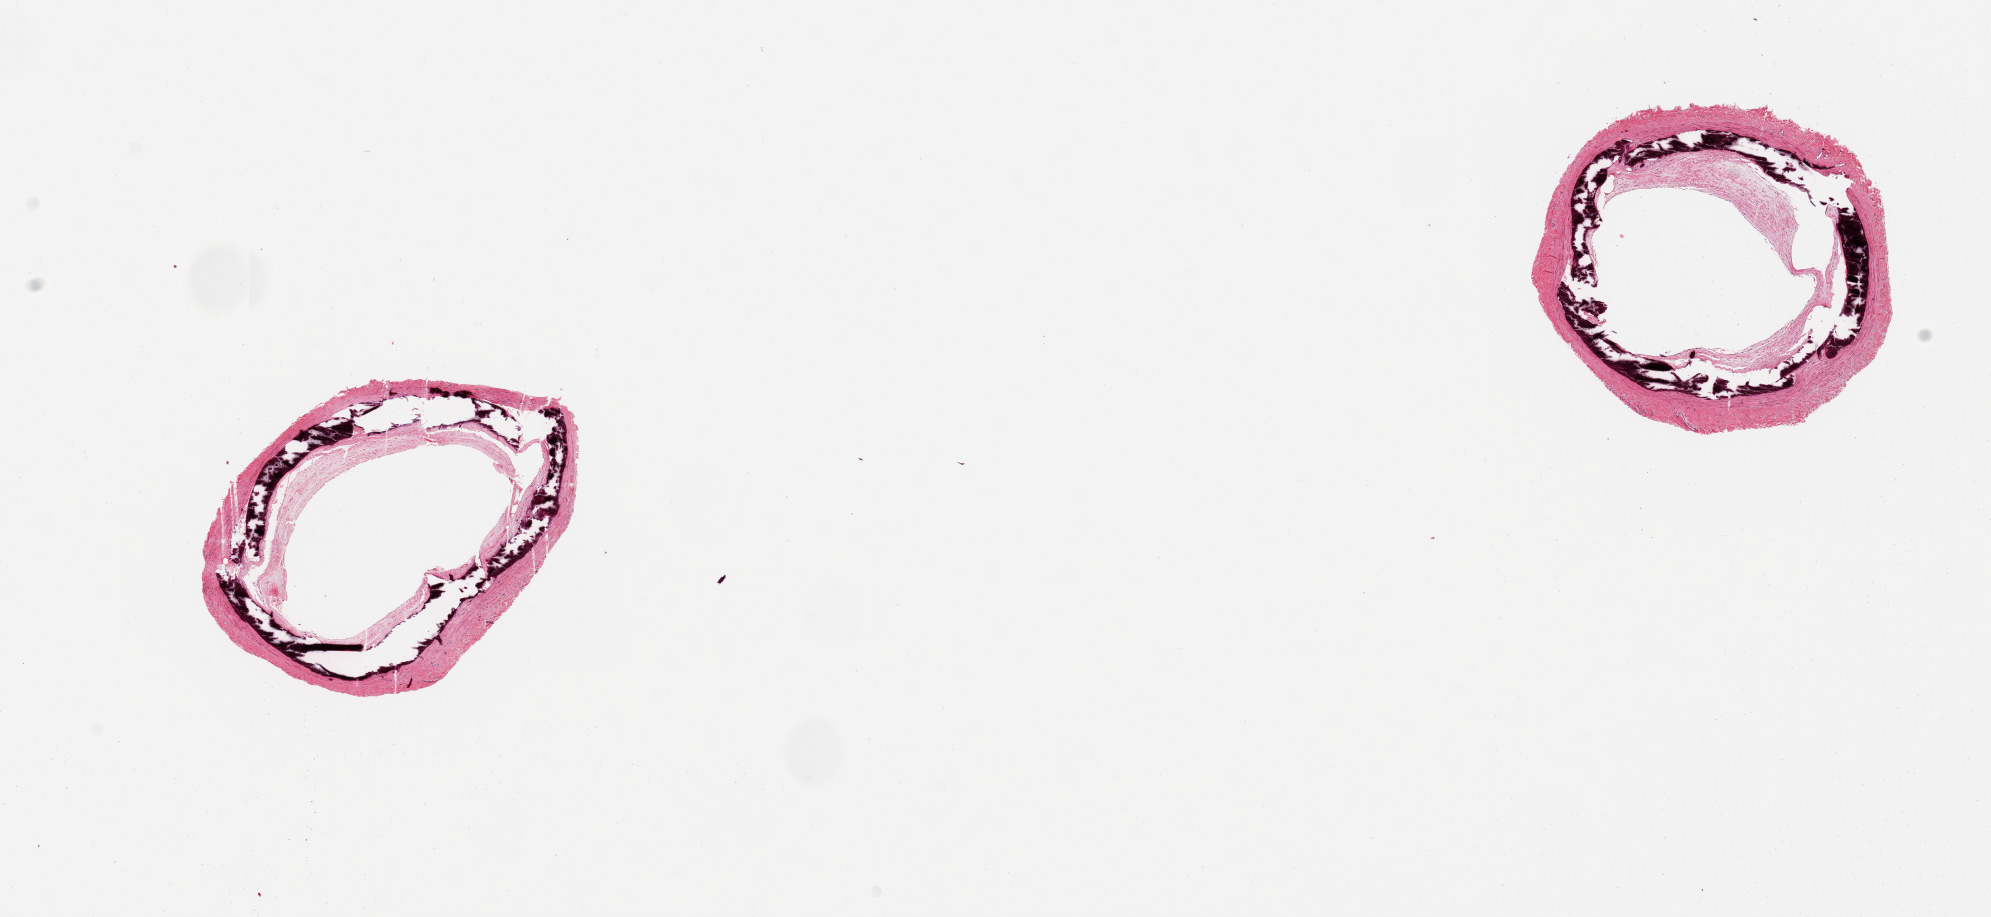
Digitized haematoxylin and eosin-stained section, whole scanned area (about 15.8 x 7.3 mm) shown as a low-resolution overview; PAXgene-fixed, paraffin-embedded tissue; target tissue: tibial artery; donor tissue sample. Donor sex: female.
Pathologist's review note for this sample: 2 pieces, atherosclerosis and medial calcific sclerosis.